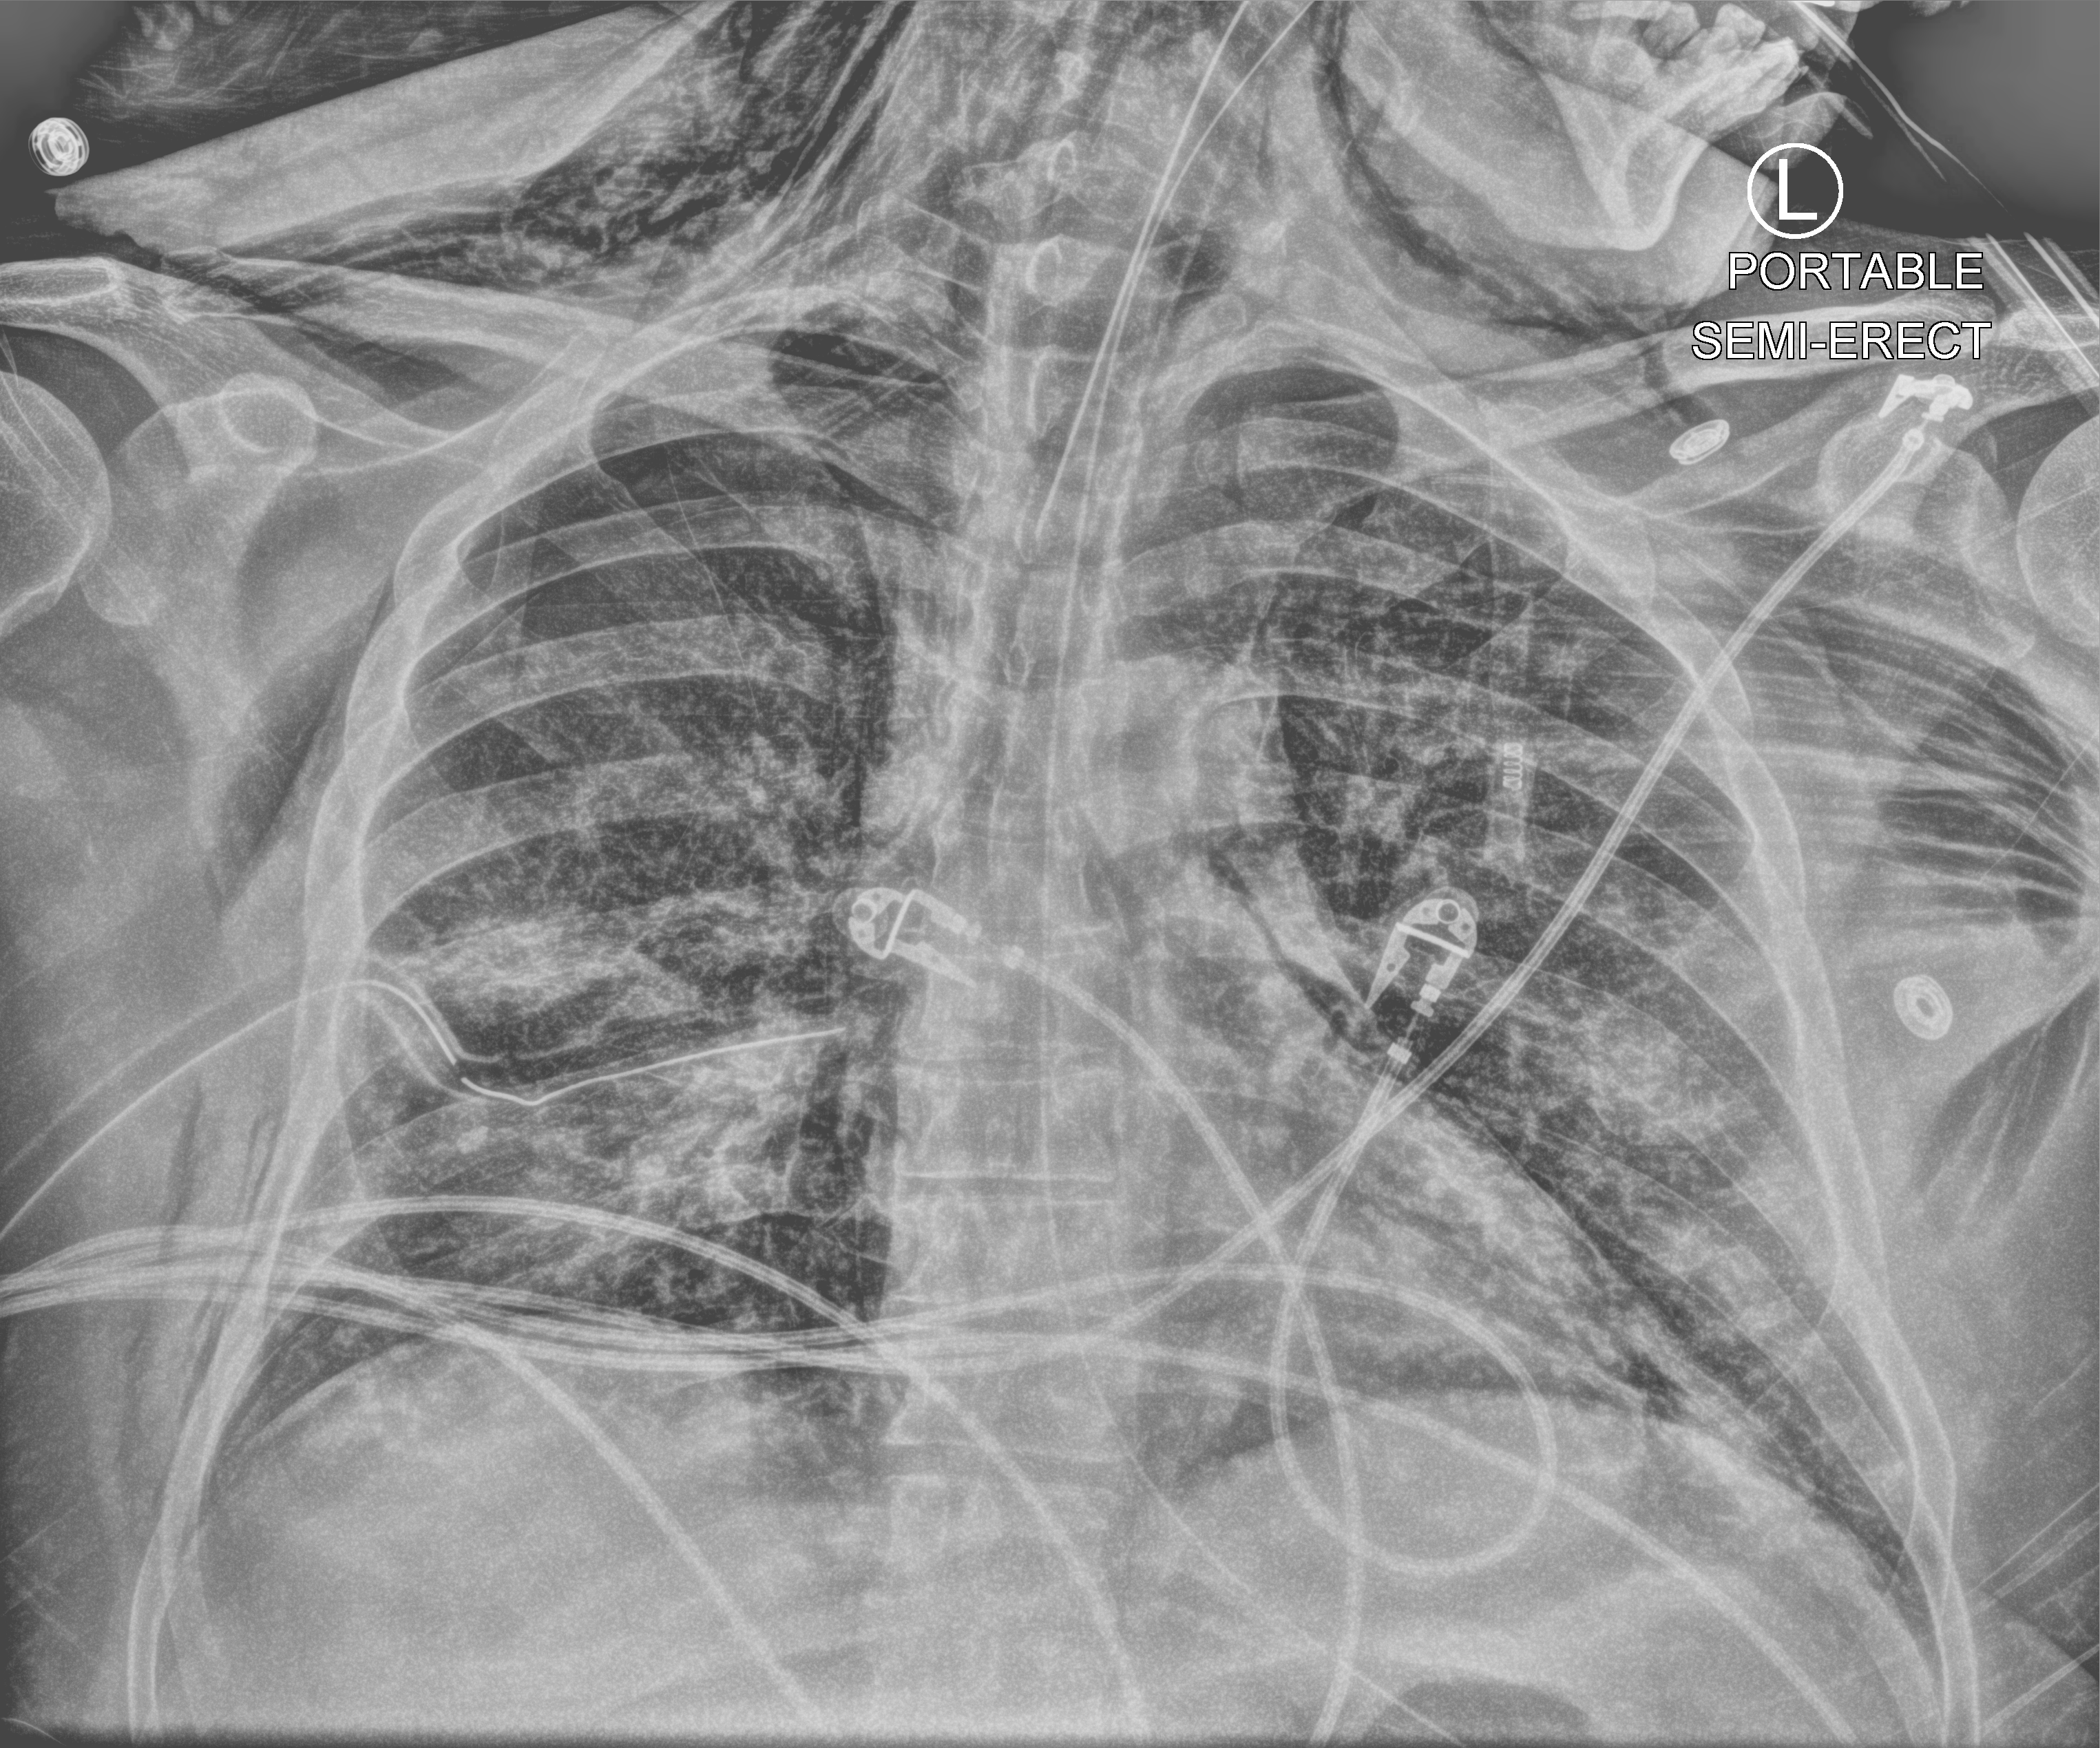
Portable chest radiograph; anteroposterior (AP) projection. Male patient hospitalised with COVID-19, age 18–59 years.
From the hospital-stay record, not from the radiograph (when in the stay this image was taken is not recorded):
- other chronic lung disease (admission record): no